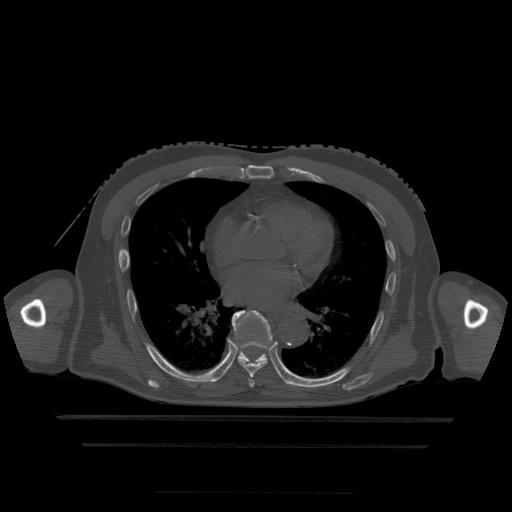
CT including the spine, one axial slice. Position 292 of 522 along the scan axis. Bone window (W 1800 / L 400 HU). 1.25 mm slice thickness. 512 × 512 image matrix. Patient age 68 years. From the clinical record (not read from this slice): primary cancer: urothelial.
Annotated regions visible in this slice (semi-automatically segmented with operator editing):
- T6 vertebra: bounding box <249,380,255,388> (left, top, right, bottom; pixels)
- T7 vertebra: <238,311,267,378>
- T8 vertebra: <232,311,283,379>